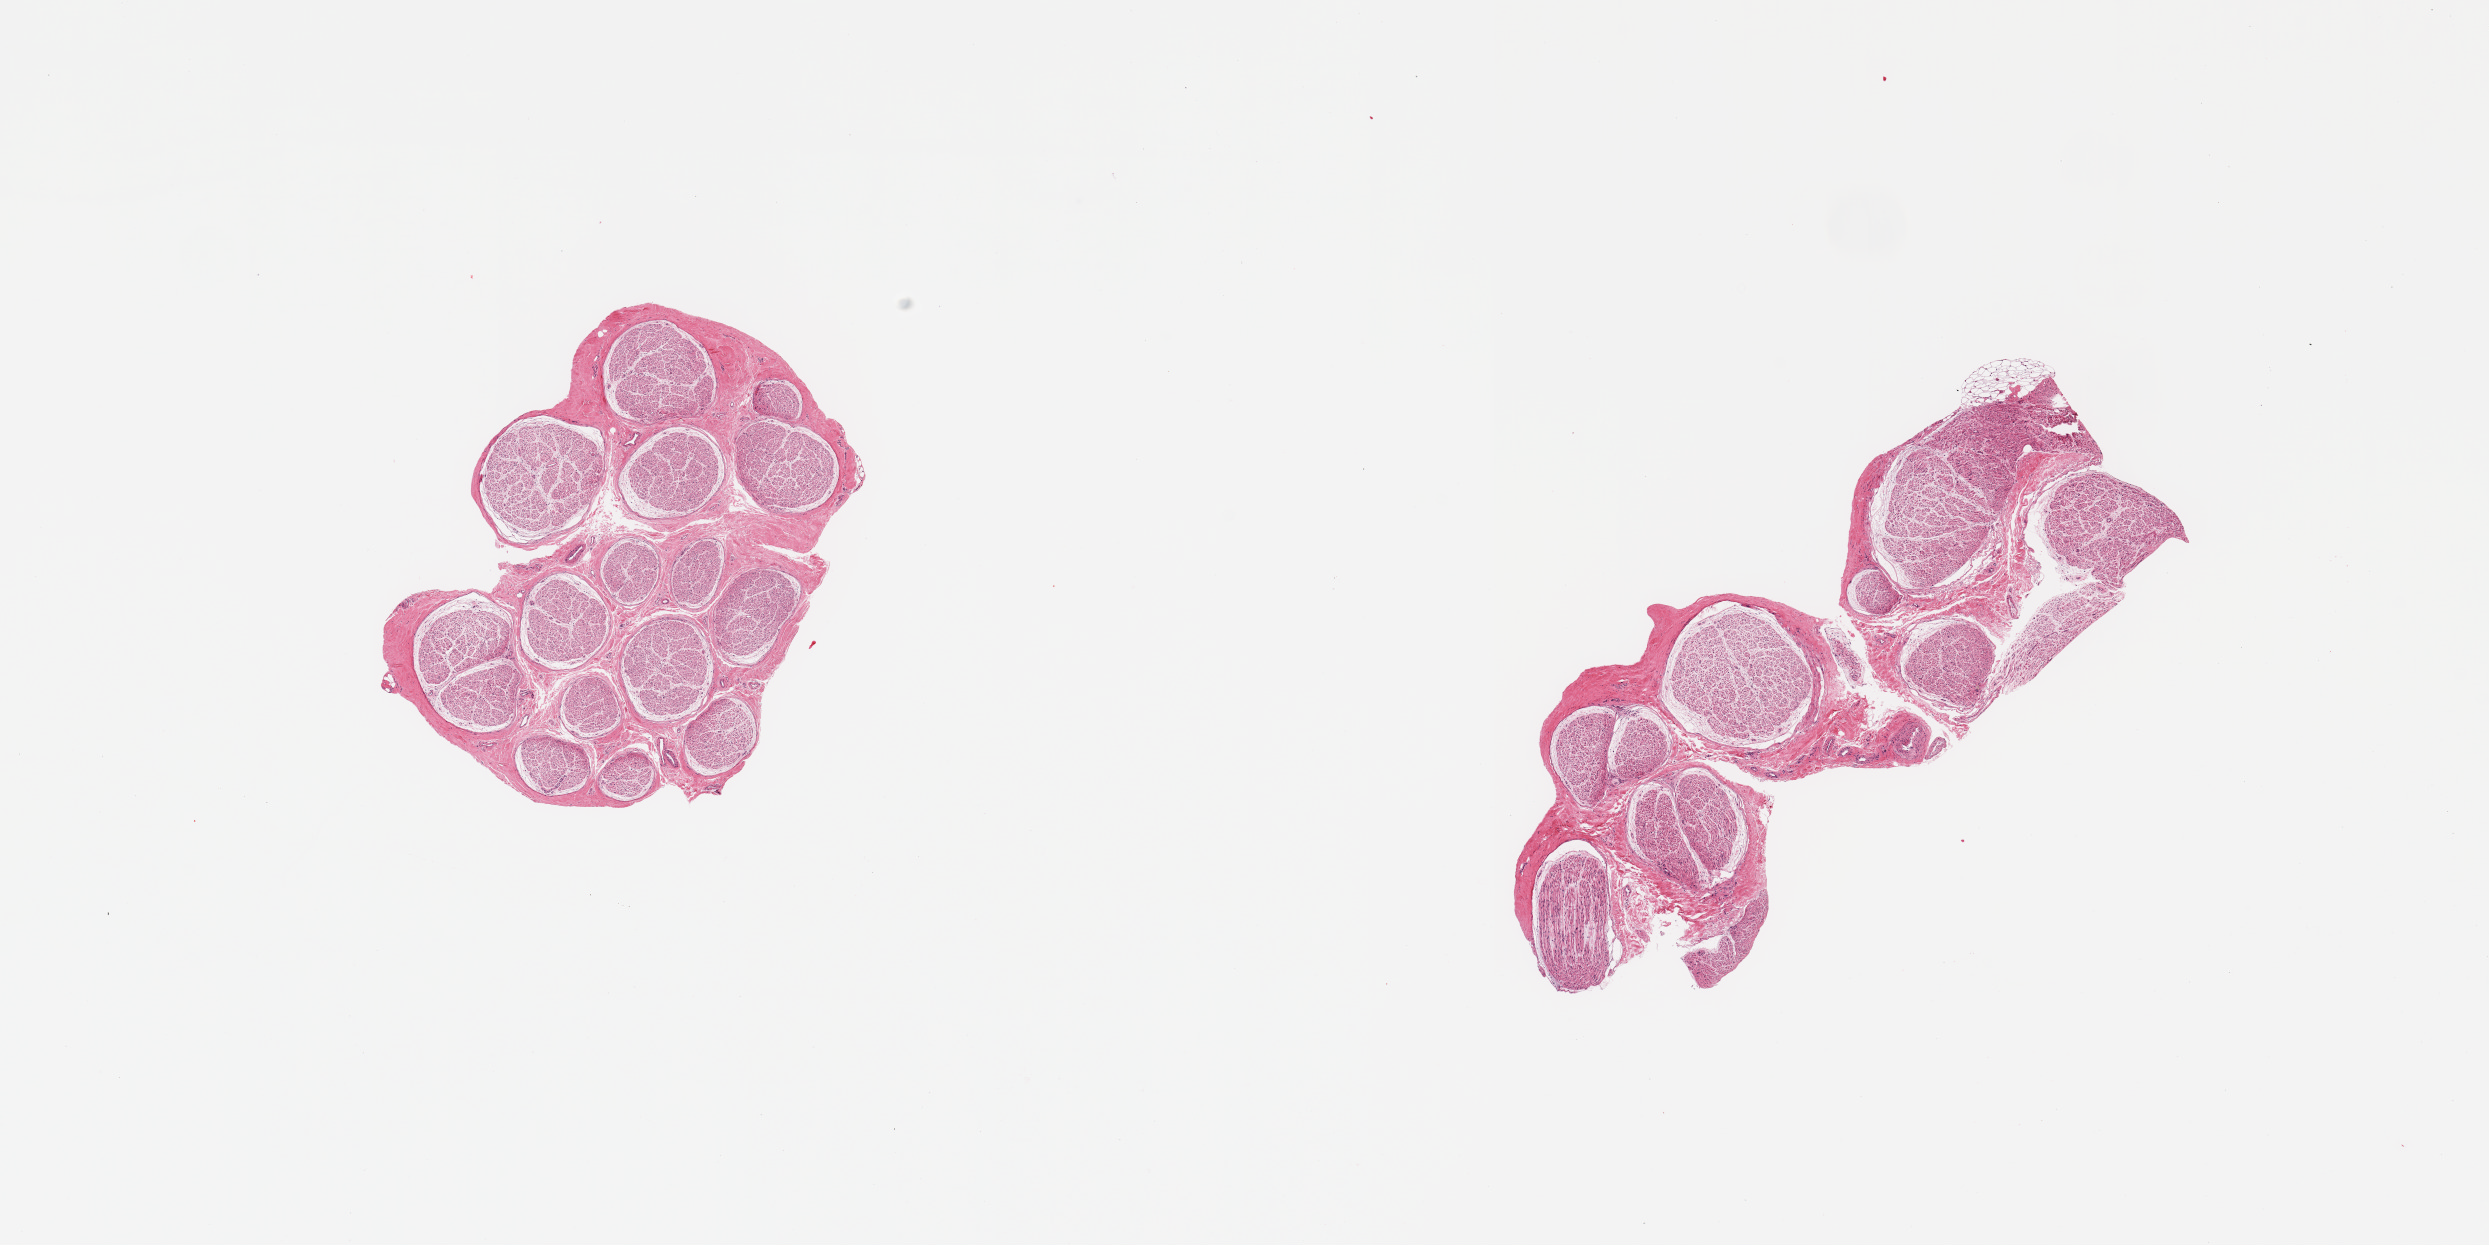
H&E whole-slide image — a low-resolution overview of the entire scanned area, about 19.7 x 9.8 mm, PAXgene-fixed paraffin-embedded (PFPE) section, sampled site (target tissue): tibial nerve, donor tissue sample.
* pathologist's review note for this sample: 2 pieces; well trimmed; virtually no internal or external fat